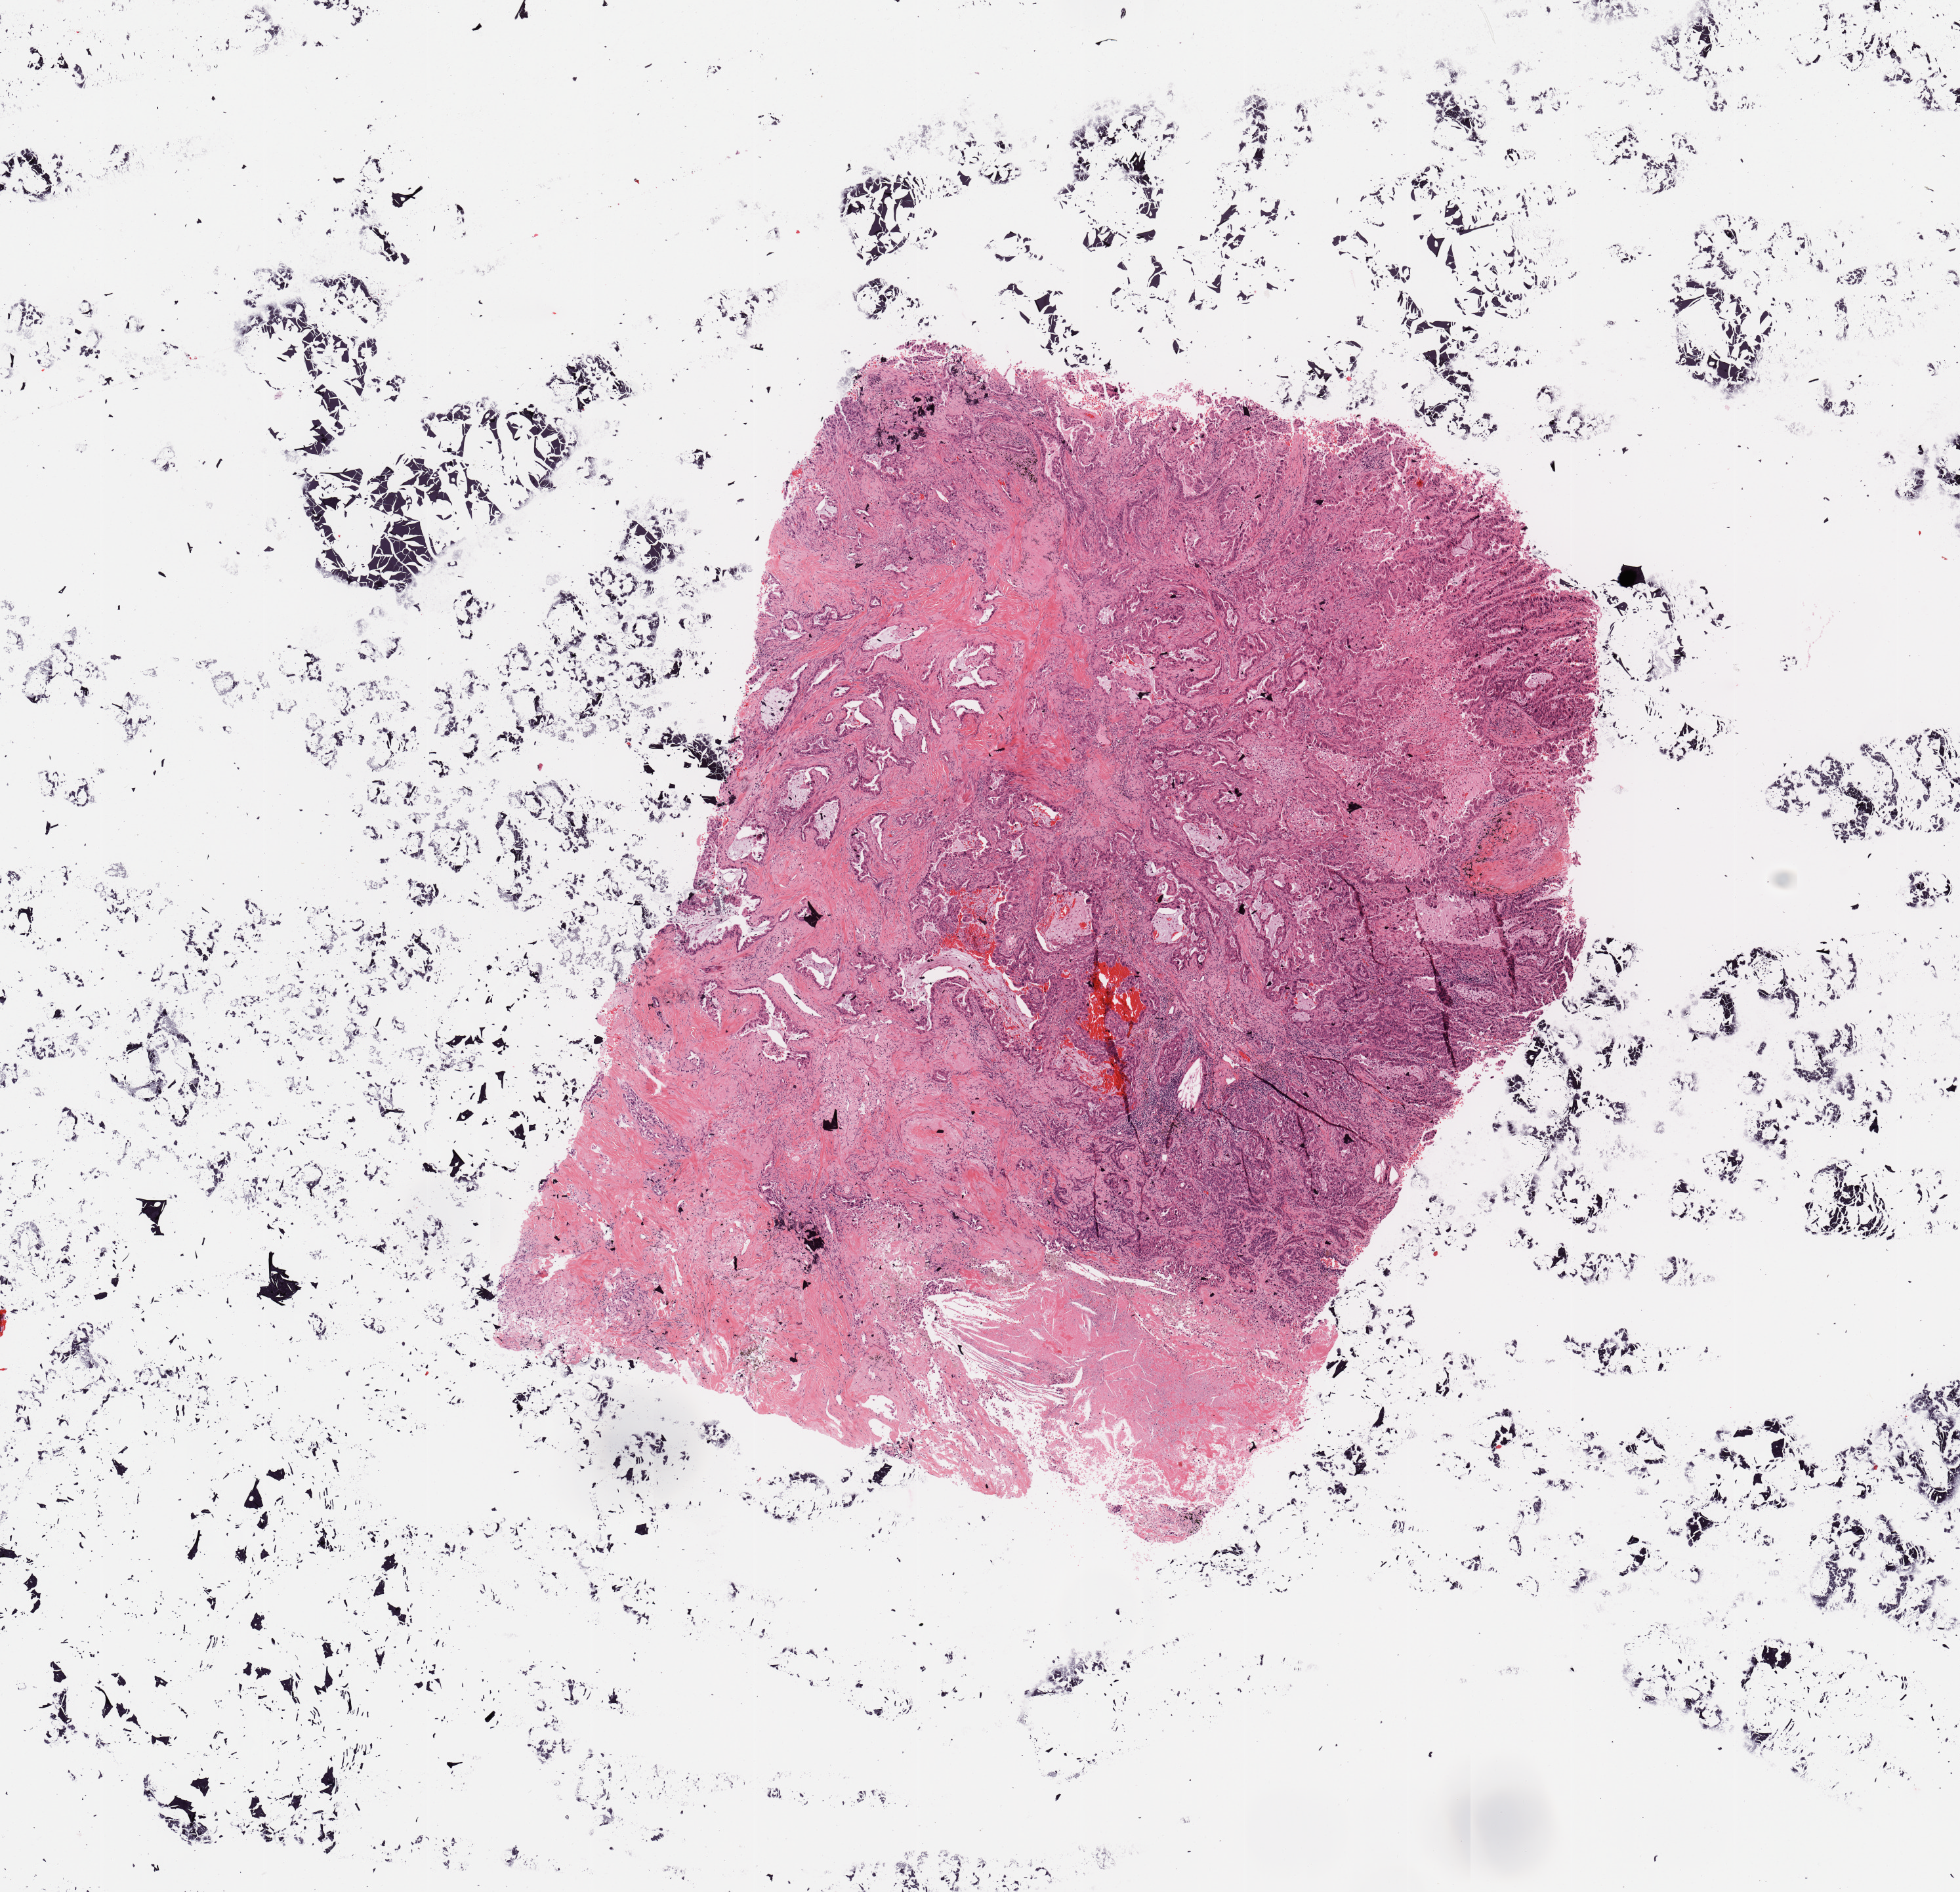
Hematoxylin and eosin (H&E) stained whole-slide image — shown as a low-resolution overview of the whole scanned area (about 11.8 x 11.4 mm); tumour tissue sample, sampled site: lung. 49-year-old male patient. Histologic grade: G3 (poorly differentiated). Composition of this section per pathologist review: tumour nuclei 70%, necrosis 10%.
* diagnosis: Adenocarcinoma, NOS
* AJCC pathologic stage: IIA
* primary tumour site (as recorded): right lower lobe